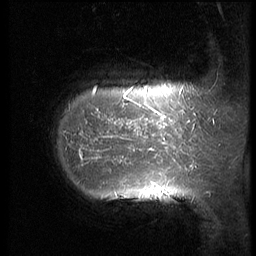
Breast MRI (dynamic contrast-enhanced), one sagittal slice; position 10 of 64 along the scan axis; 3 images stored at this slice position (order not interpretable as contrast timing); 1.5 T; TE 4.2 ms, TR 9 ms; 2.5 mm slice thickness; 256 × 256 image matrix, field of view 180 × 180 mm. Female patient, age 39 years. From the clinical record (not read from this slice): setting: breast cancer imaged before/during neoadjuvant chemotherapy; receptor status: HER2-positive.
Outlined on this slice (semi-automatically segmented with operator editing):
- analysis volume of interest (the breast-tissue region the enhancement analysis was run in; not a lesion): bounding box (x1, y1, x2, y2) in pixels: (45, 57, 210, 239)
- tumour enhancement mask (voxels above the 140 % enhancement threshold inside the analysis volume of interest): (79, 97, 174, 170)